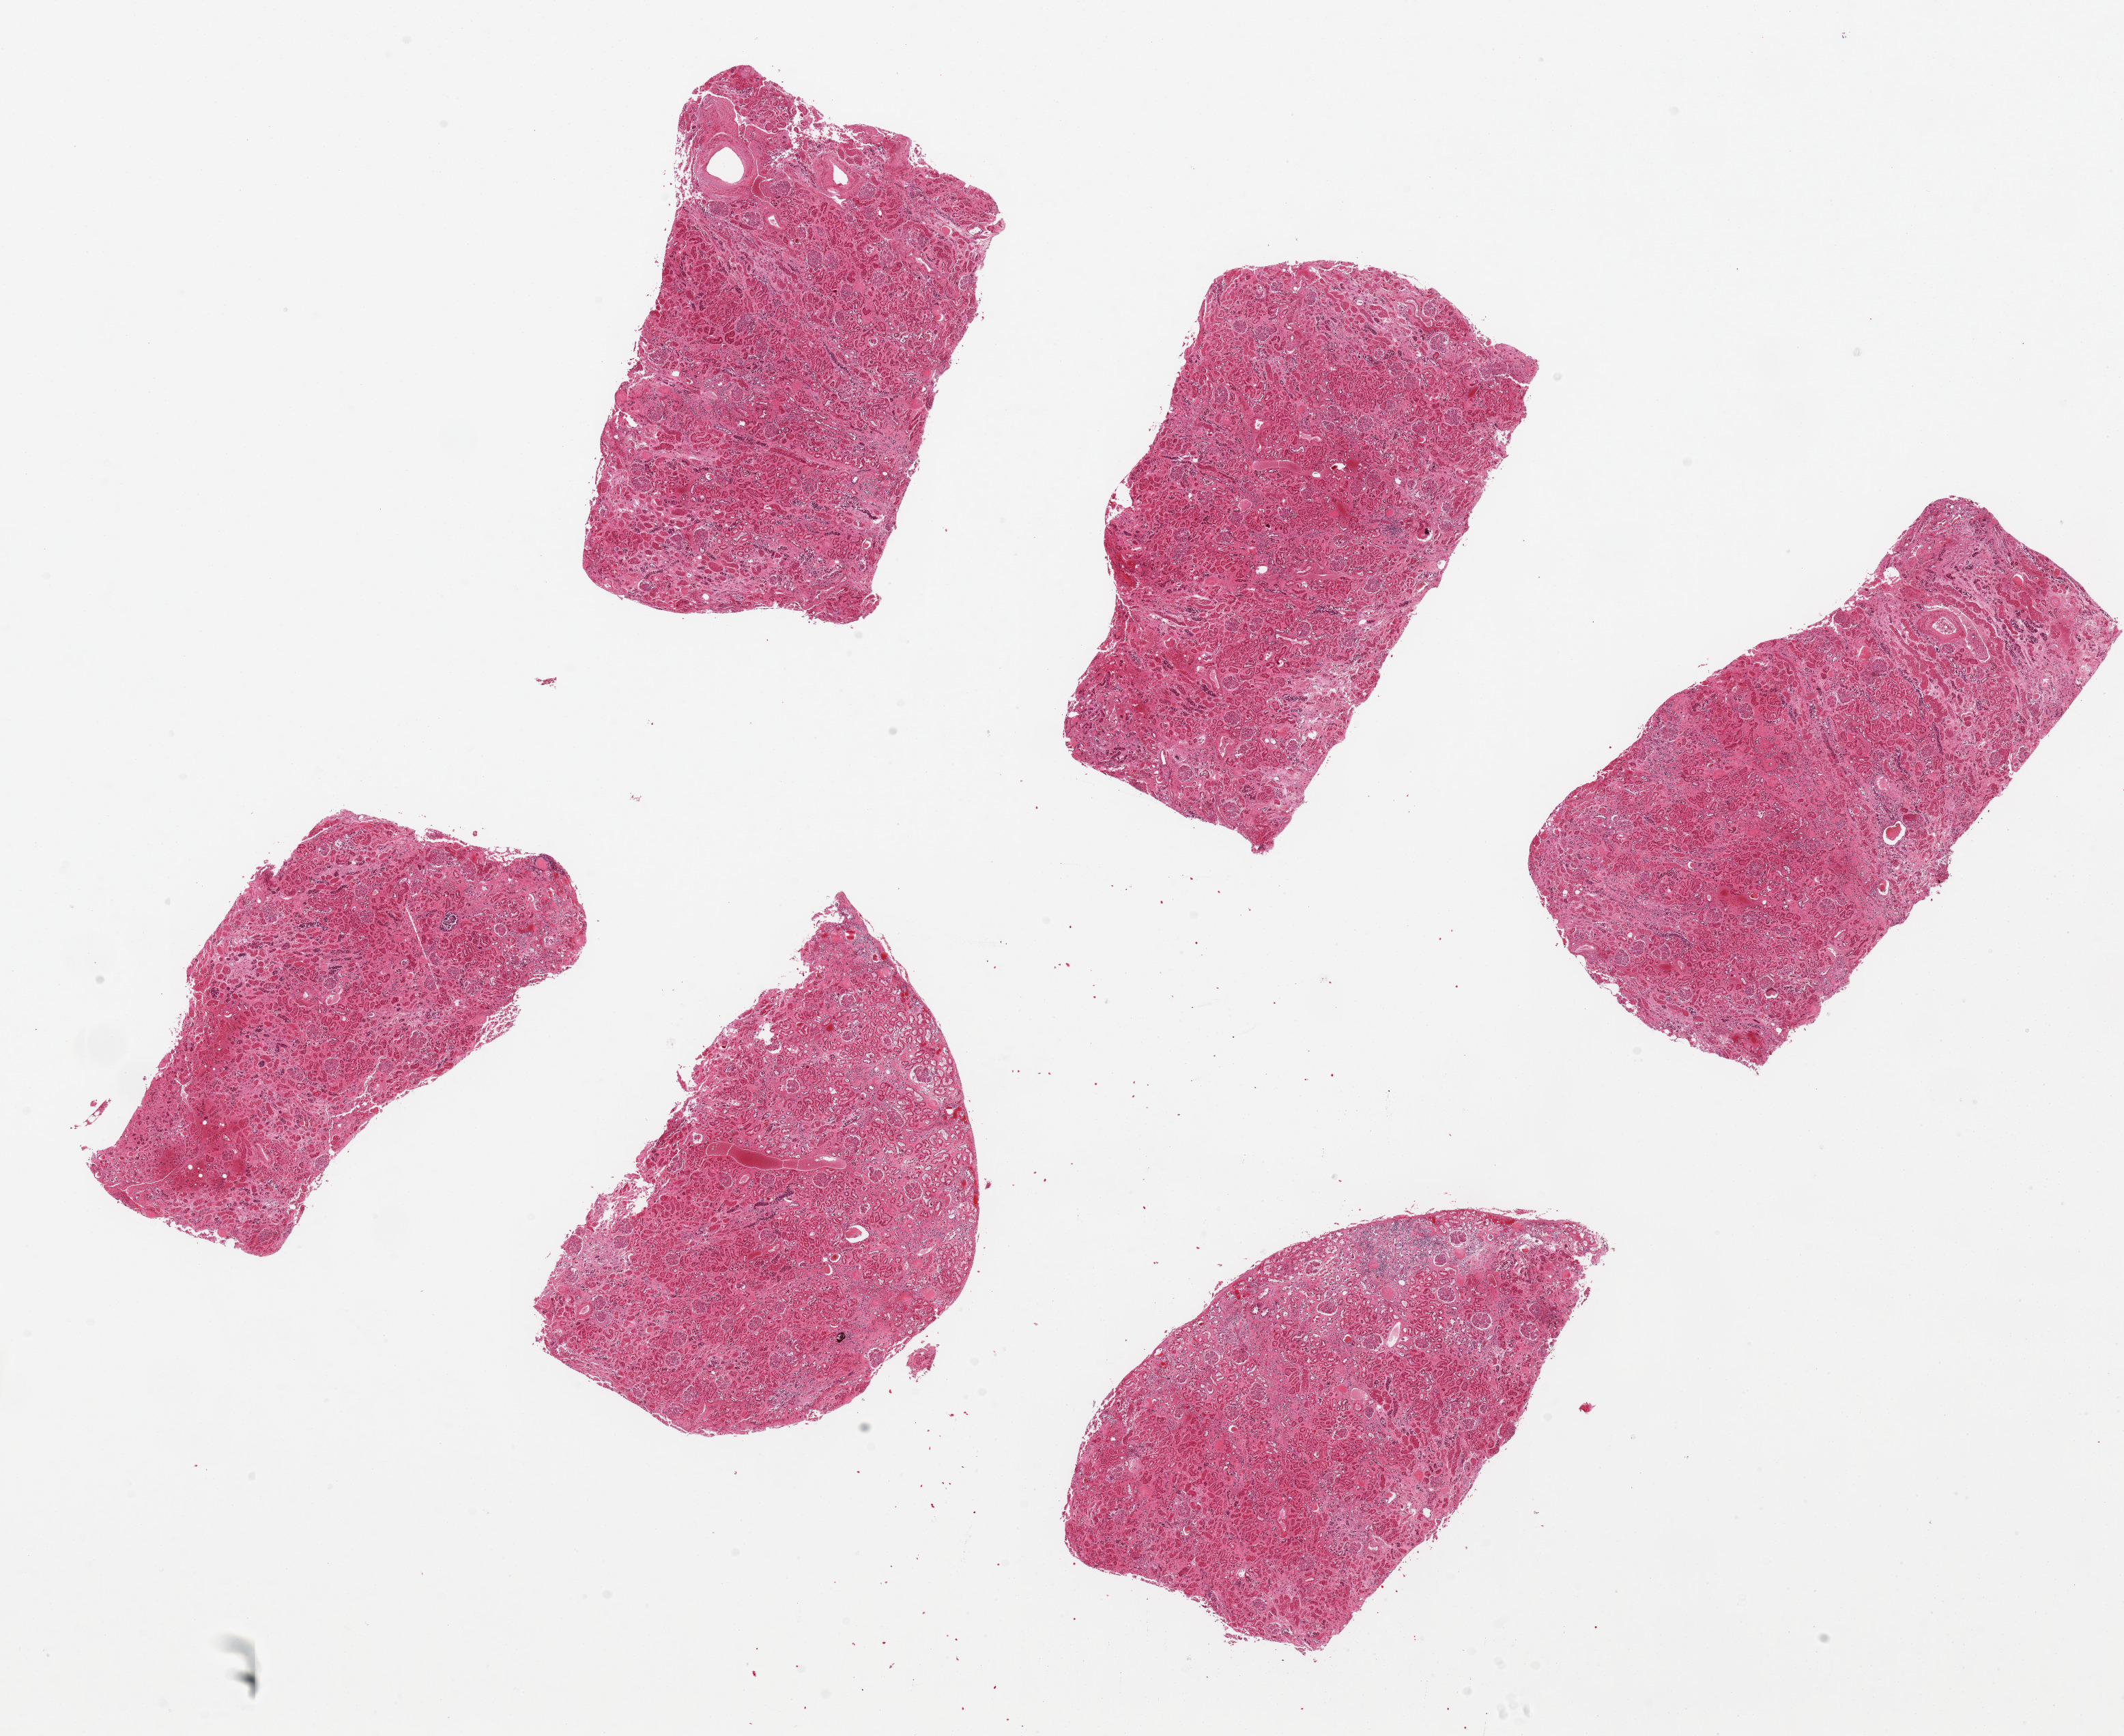
Digitized haematoxylin and eosin-stained section — low-resolution overview of the scanned area, about 24.6 x 20.1 mm (acquisition: 20x scan), PAXgene-fixed paraffin-embedded (PFPE) section, target tissue: renal cortex, donor tissue sample.
• review note (as recorded): 6 pieces ~7x3. Tubules badly autolyzed